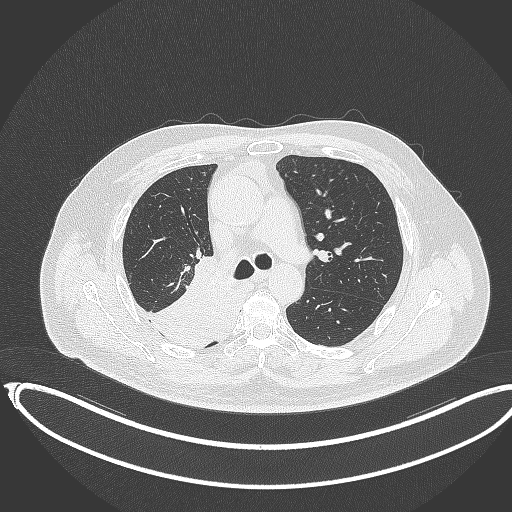
Chest CT, one axial slice. Reconstruction kernel B70f. 120 kVp. Lung window (W 1500 / L -600 HU). 512 × 512 image matrix, field of view 436 × 436 mm. Male patient, age 68 years. From the clinical record (not read from this slice): clinical TNM (as recorded): T2a N0 M0.
Structures marked on this image (rectangle marked by the reading radiologist):
- lung tumour (recorded histology: adenocarcinoma): box from (x=145, y=262) to (x=242, y=351) px